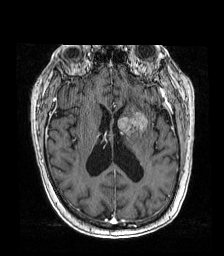
Brain MRI from a brain-tumour surgery series, one axial slice. Position 78 of 192 along the scan axis. T1-weighted post-contrast. 224 × 256 image matrix, field of view 219 × 250 mm. From the clinical record (not read from this slice): histopathology: Metastatic carcinoma from lung primary; tumour location: Left Frontal Caudate.
Outlined on this slice (outlined manually by an expert reader):
- tumour: bounding box [x1, y1, x2, y2] px = [117, 110, 148, 137]